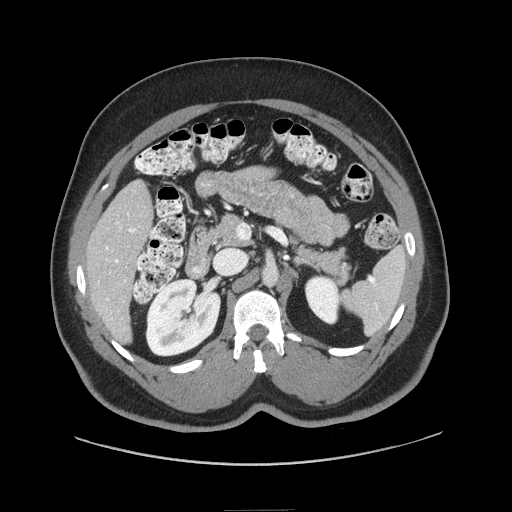
Contrast-enhanced abdominal CT (liver protocol), one axial slice; position 32 of 87 along the scan axis; reconstruction kernel STANDARD; soft-tissue window (W 400 / L 40 HU); 2.5 mm slice thickness; 512 × 512 image matrix, field of view 440 × 440 mm. From the clinical record (not read from this slice): diagnosis: hepatocellular carcinoma (patient treated with transarterial chemoembolisation; whether this scan precedes or follows treatment is not stated here); TNM stage (as recorded): Stage-II; Child-Pugh class: A; tumour differentiation: moderately differentiated; tumour nodularity: uninodular.
Outlined on this slice (semi-automatically segmented with operator editing):
- liver parenchyma outside the tumour (the mass and vessels are separate outlines, so this box may not span the whole liver): bounding box (x1, y1, x2, y2) in pixels: (86, 180, 152, 342)
- liver vessels: (105, 213, 136, 320)